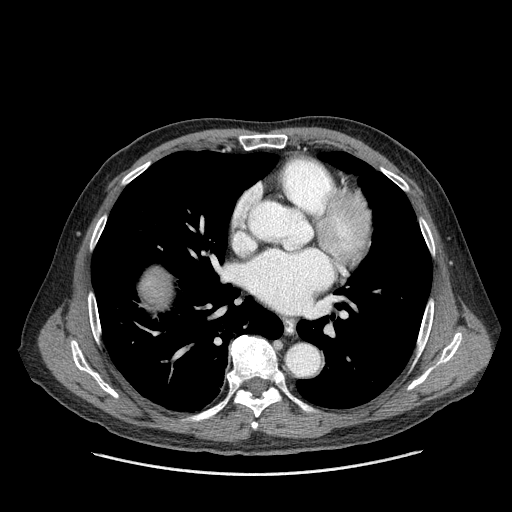
Contrast-enhanced abdominal CT (liver protocol), one axial slice. Slice 168 of 180 in the series (ordered by position). 120 kVp. One of 2 acquisitions stored at this slice position. Soft-tissue window (W 400 / L 40 HU). 512 × 512 image matrix, field of view 420 × 420 mm. From the clinical record (not read from this slice): diagnosis: hepatocellular carcinoma (patient treated with transarterial chemoembolisation; whether this scan precedes or follows treatment is not stated here); TNM stage (as recorded): Stage-II; Child-Pugh class: A; tumour differentiation: well differentiated; tumour nodularity: multinodular.
Annotated regions visible in this slice (semi-automatic segmentation, software-assisted and operator-edited):
- liver parenchyma outside the tumour (the mass and vessels are separate outlines, so this box may not span the whole liver): bounding box [x1, y1, x2, y2] px = [140, 268, 172, 308]